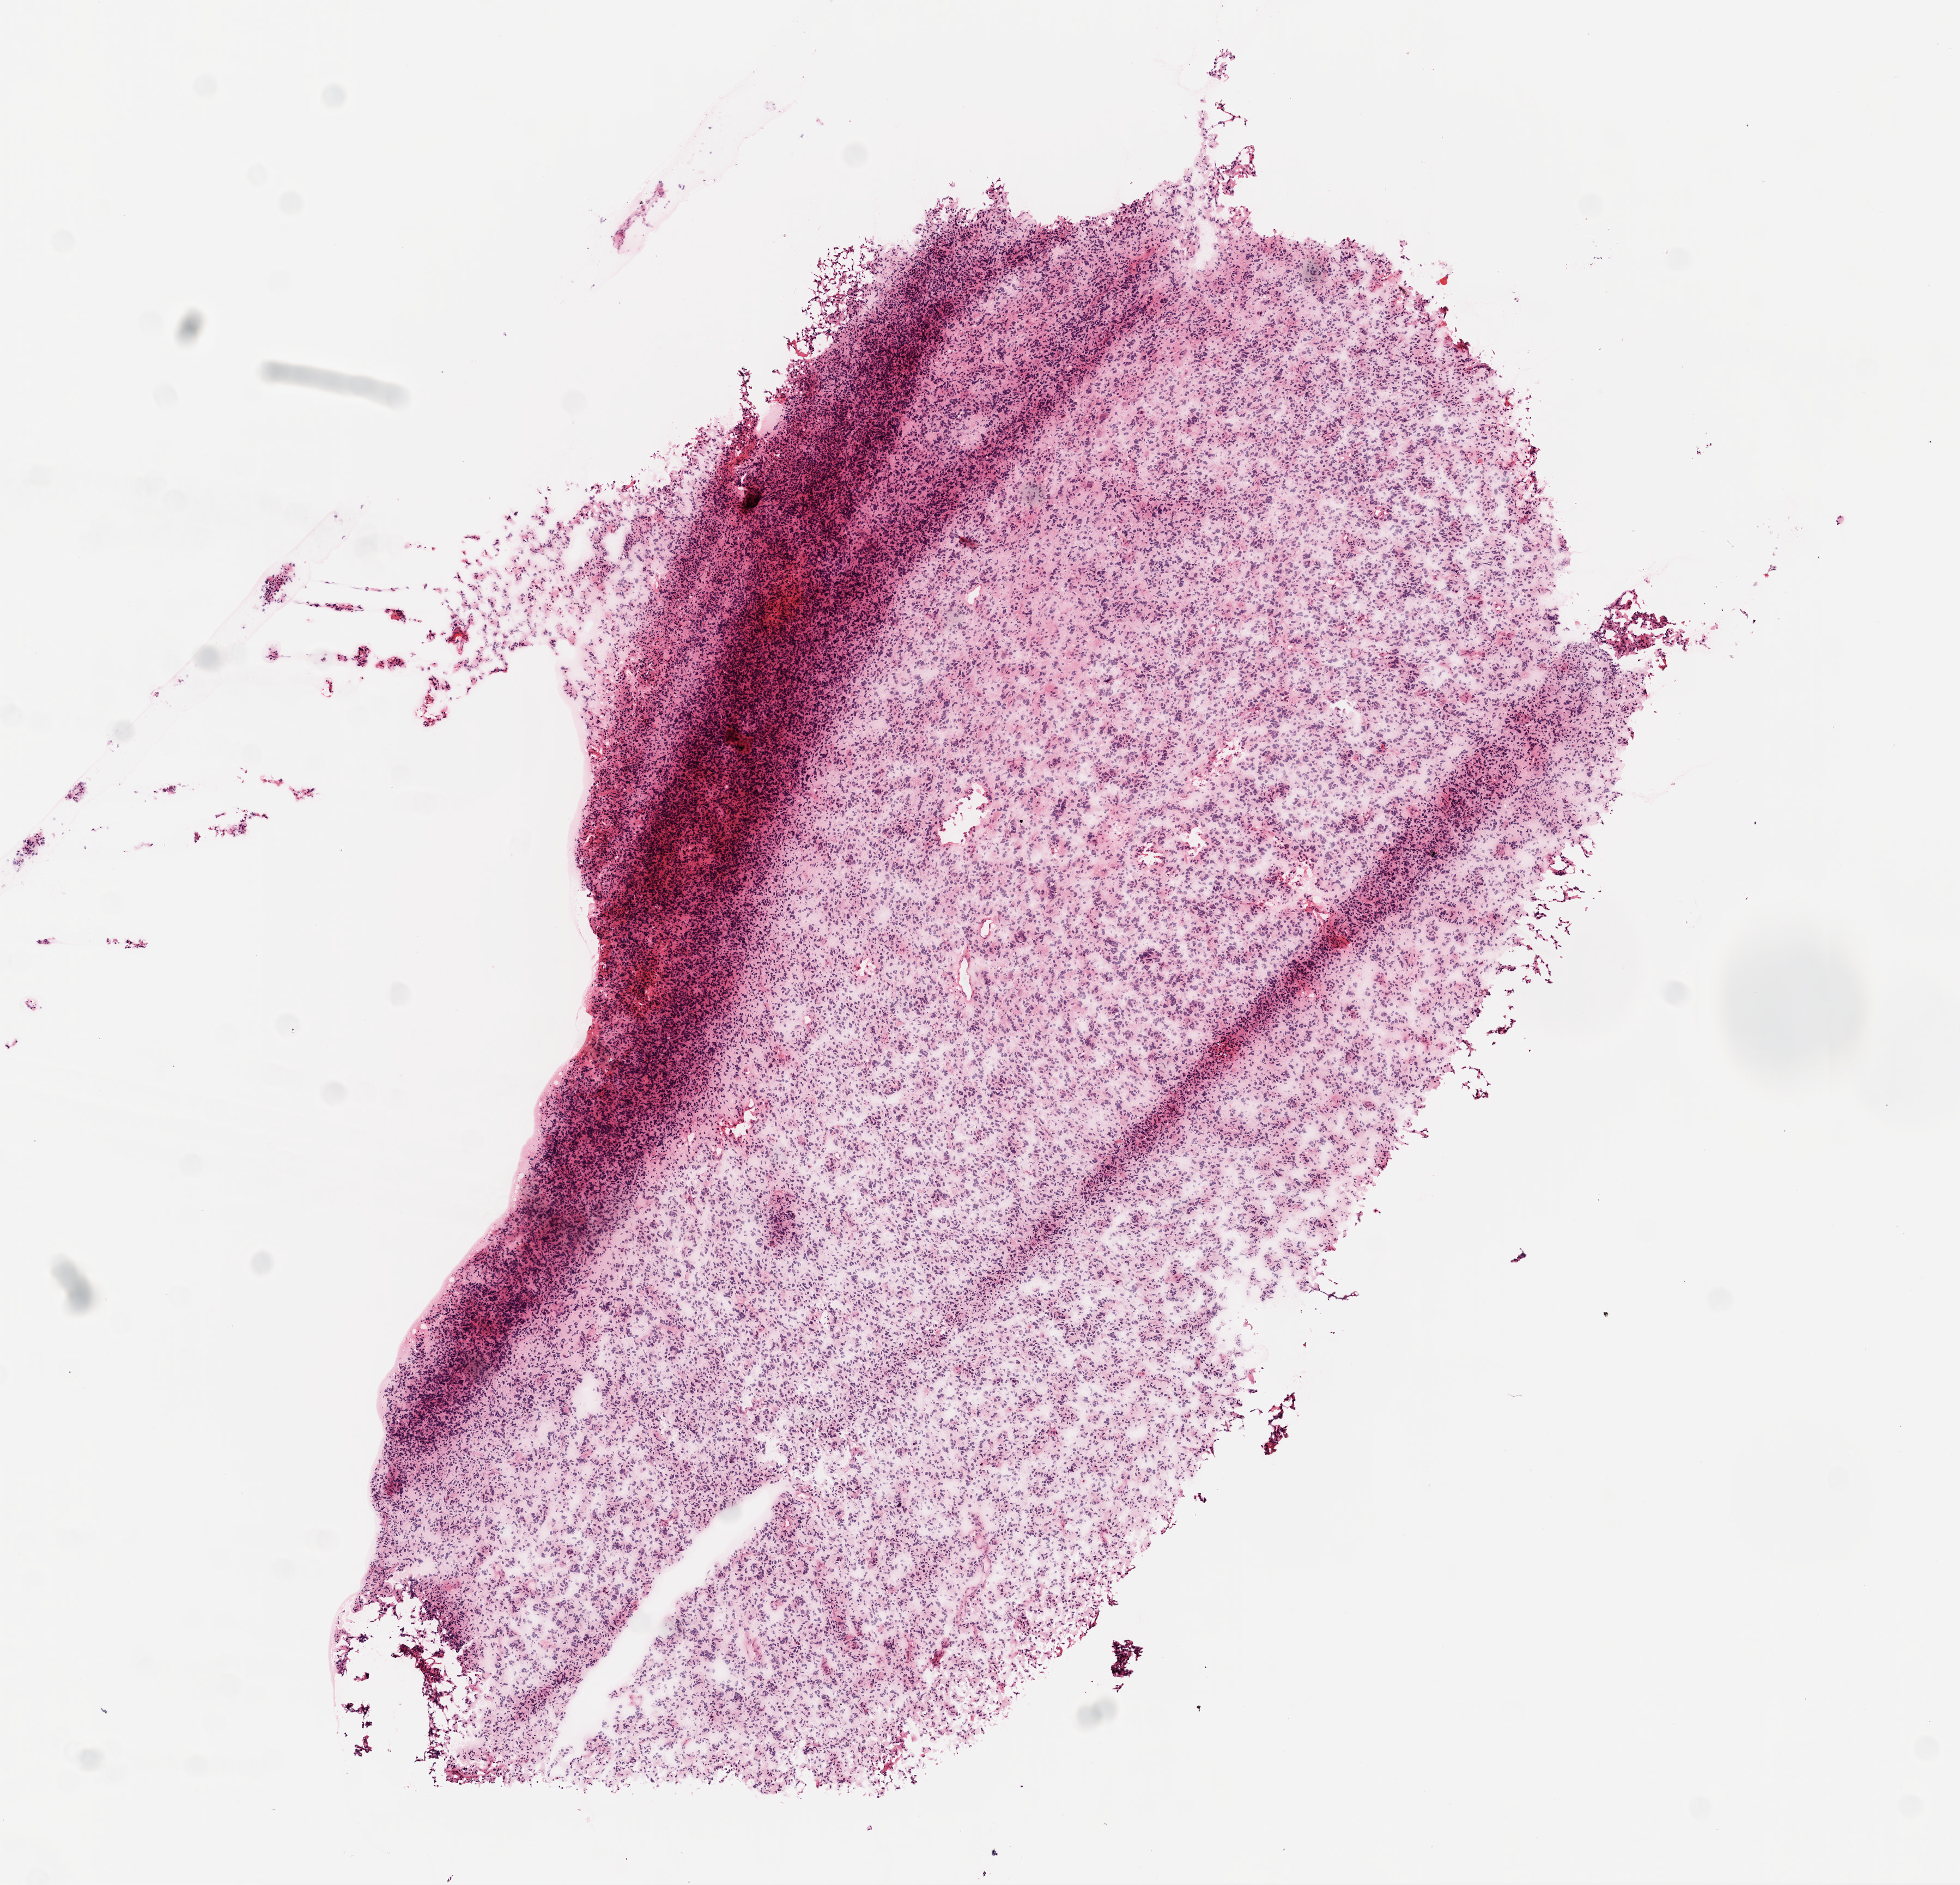
Whole-slide histology image, H&E-stained, a low-resolution overview of the entire scanned area, about 7.3 x 7.0 mm, frozen section from the top of the tissue portion, primary tumour sample from the brain. Male, age 66 years at initial diagnosis. Pathologist review of this section (percent, as recorded): tumour cells 100%, tumour nuclei 95%, normal cells 0%, stromal cells 0%, necrosis 0%.
Diagnosis: Glioblastoma.